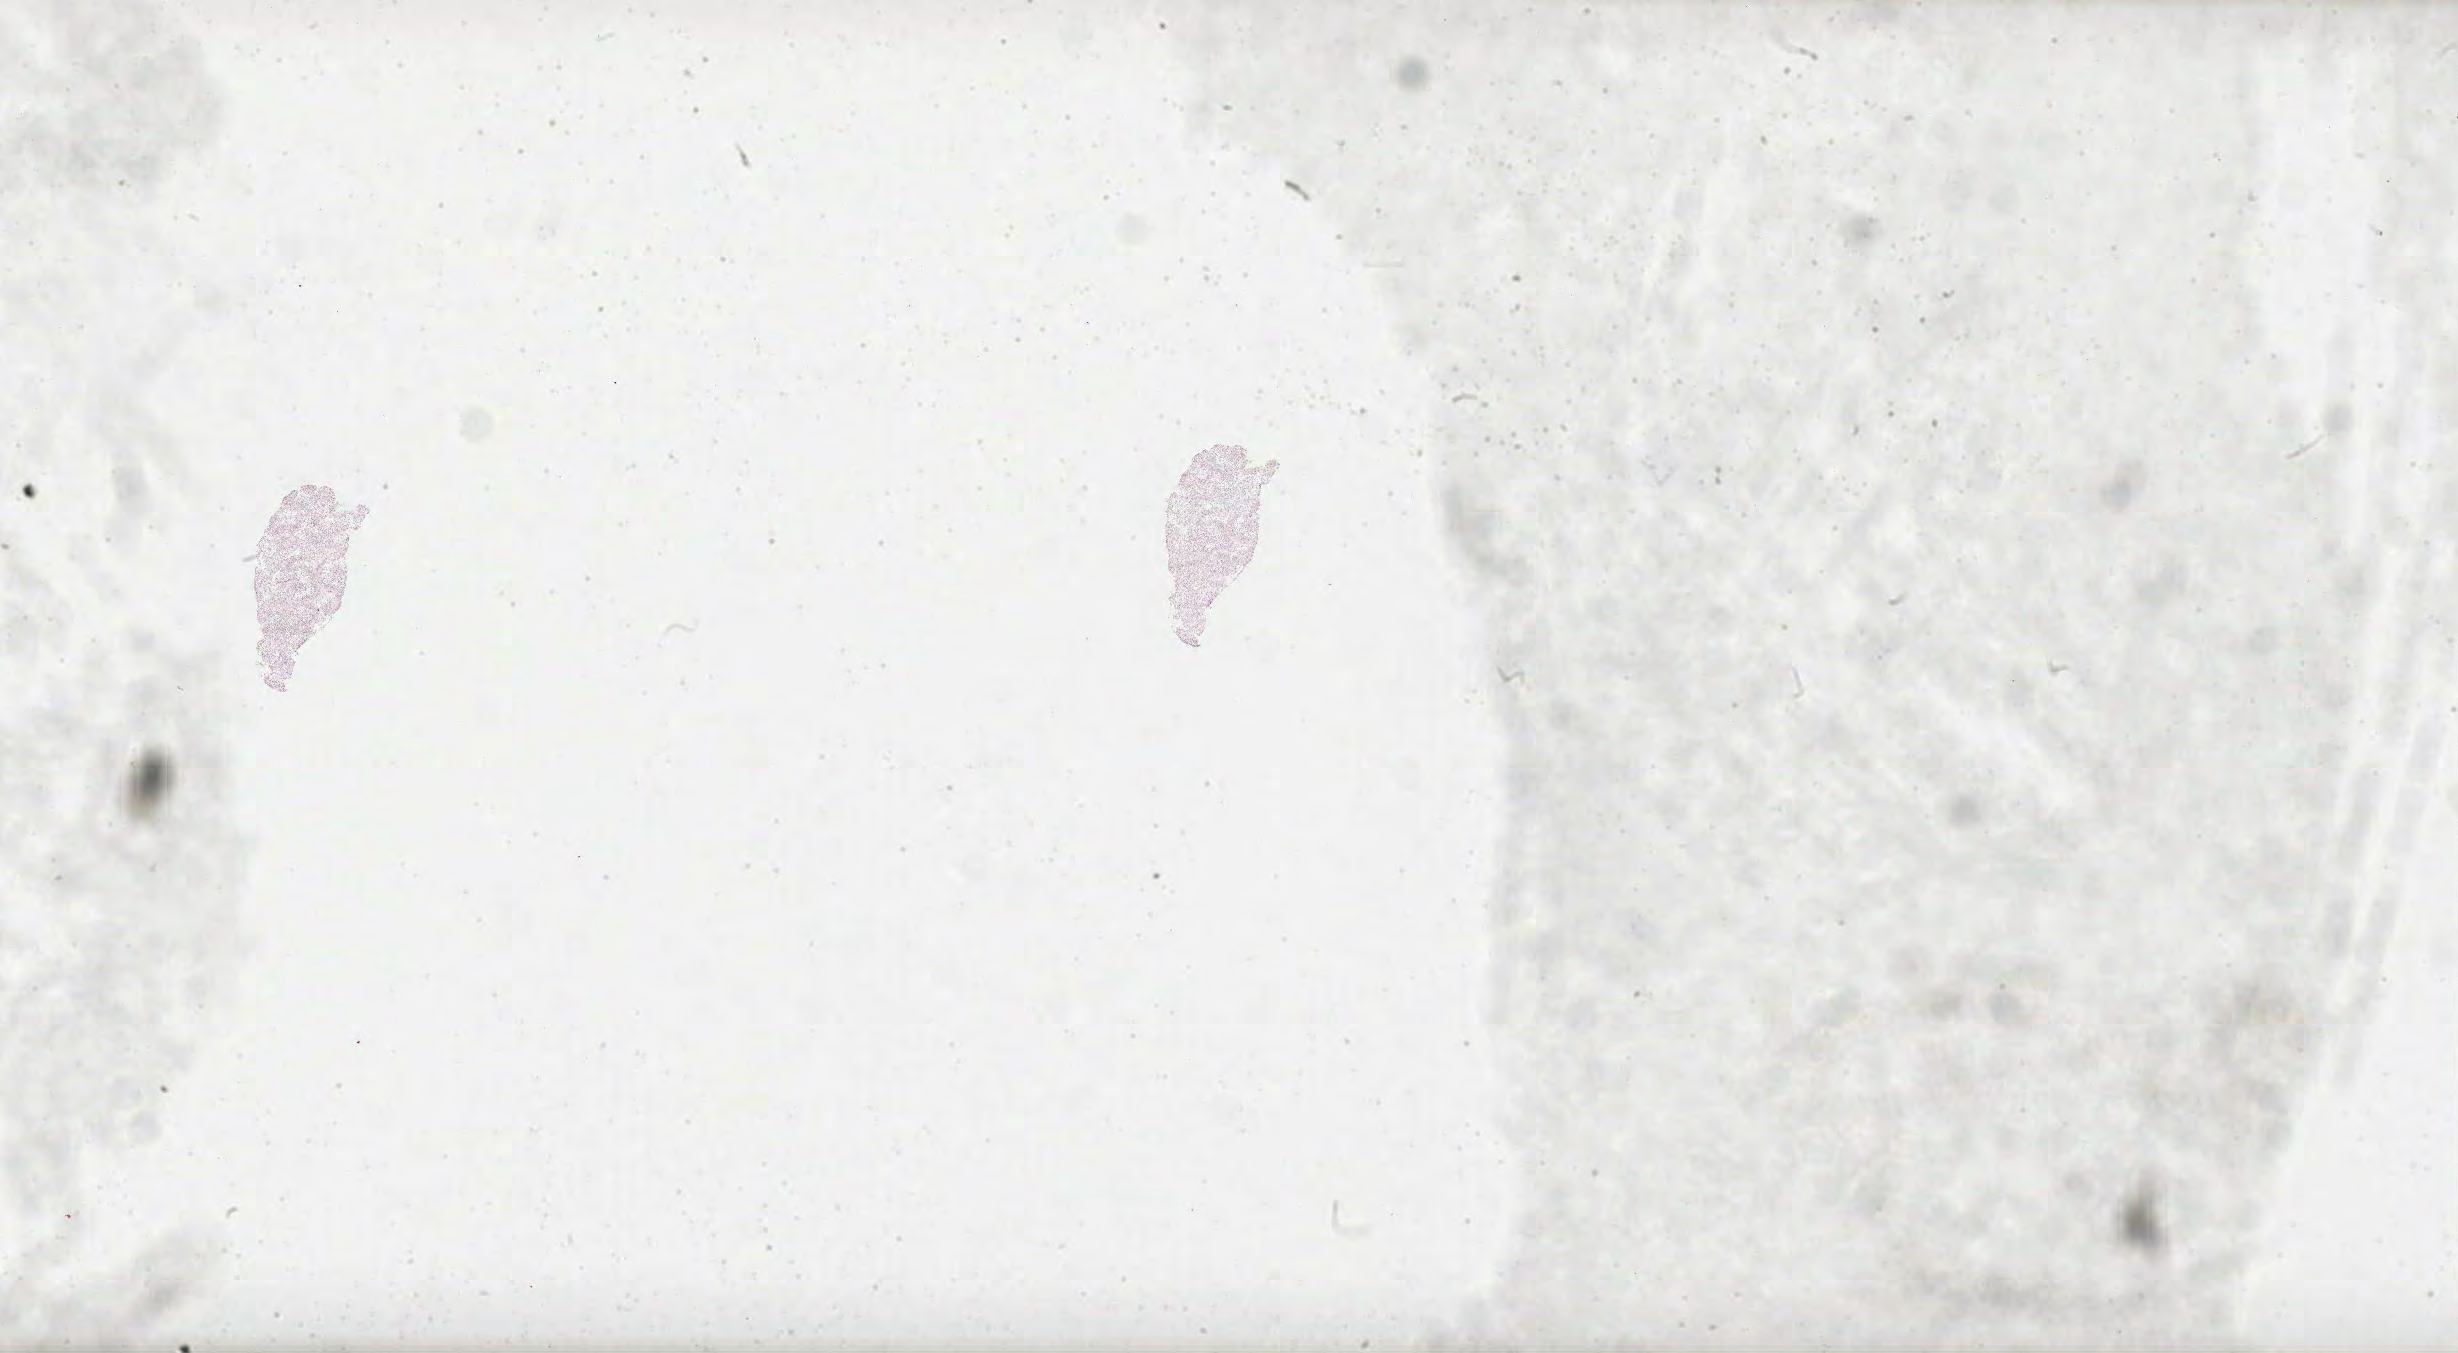
Digitized Hematoxylin and eosin (H&E) stained tissue section (whole slide) — whole scanned area (about 39.6 x 21.8 mm, acquisition: 40x scan) shown as a low-resolution overview; formalin-fixed paraffin-embedded (FFPE) diagnostic section; primary tumour sample from the brain. Male, age 56 years at initial diagnosis.
• pathologic diagnosis: Glioblastoma